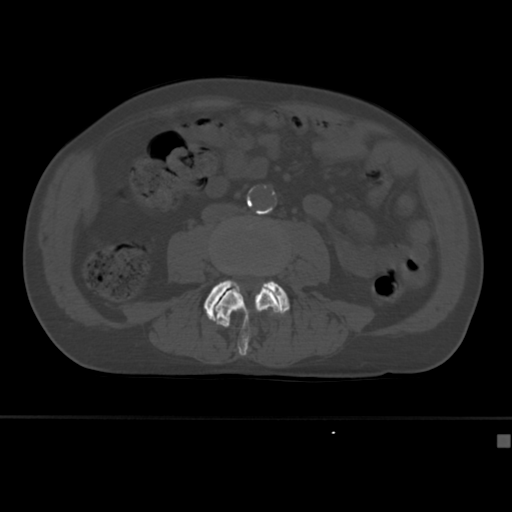
CT including the spine, one axial slice. Position 117 of 430 along the scan axis. Reconstruction kernel Br40s. 120 kVp. Bone window (W 1800 / L 400 HU). 1.5 mm slice thickness. 512 × 512 image matrix, field of view 337 × 337 mm. Male patient, age 64 years. From the clinical record (not read from this slice): primary cancer: uterus; vertebrae with lytic lesions (as recorded): T1, T4, T5, T7, L5.
Outlined on this slice (semi-automatically segmented with operator editing):
- L3 vertebra: box from (x=215, y=289) to (x=280, y=356) px
- L4 vertebra: (x=204, y=267)–(x=290, y=327)